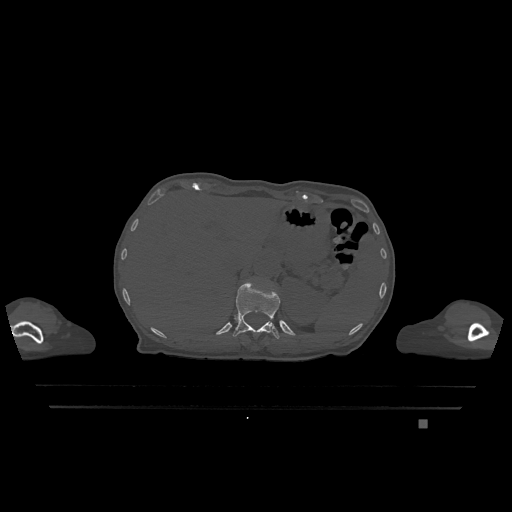
CT including the spine, one axial slice; position 532 of 1317 along the scan axis; bone window (W 1800 / L 400 HU); 512 × 512 image matrix. Patient: female, 74 years. Case-level facts recorded for this patient, not image findings: primary cancer: lung; vertebrae with lytic lesions (as recorded): T1, T4, T5, T6, L4, L5.
Annotated regions visible in this slice (semi-automatic segmentation, software-assisted and operator-edited):
- T12 vertebra: box from (x=233, y=282) to (x=280, y=339) px